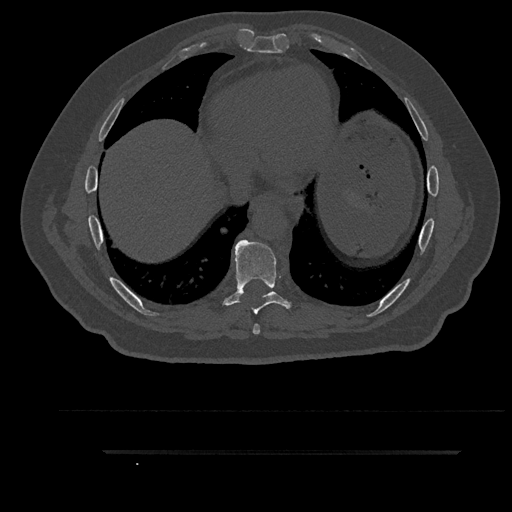
CT including the spine, one axial slice. Position 477 of 797 along the scan axis. Reconstruction kernel Br40s/3. 120 kVp. Bone window (W 1800 / L 400 HU). 512 × 512 image matrix, field of view 432 × 432 mm. Male patient, age 63 years. Case-level facts recorded for this patient, not image findings: primary cancer: renal; vertebrae with lytic lesions (as recorded): T8.
Structures marked on this image (semi-automatically segmented with operator editing):
- T7 vertebra: bounding box (x1, y1, x2, y2) in pixels: (253, 324, 260, 335)
- T8 vertebra: (217, 239, 296, 314)